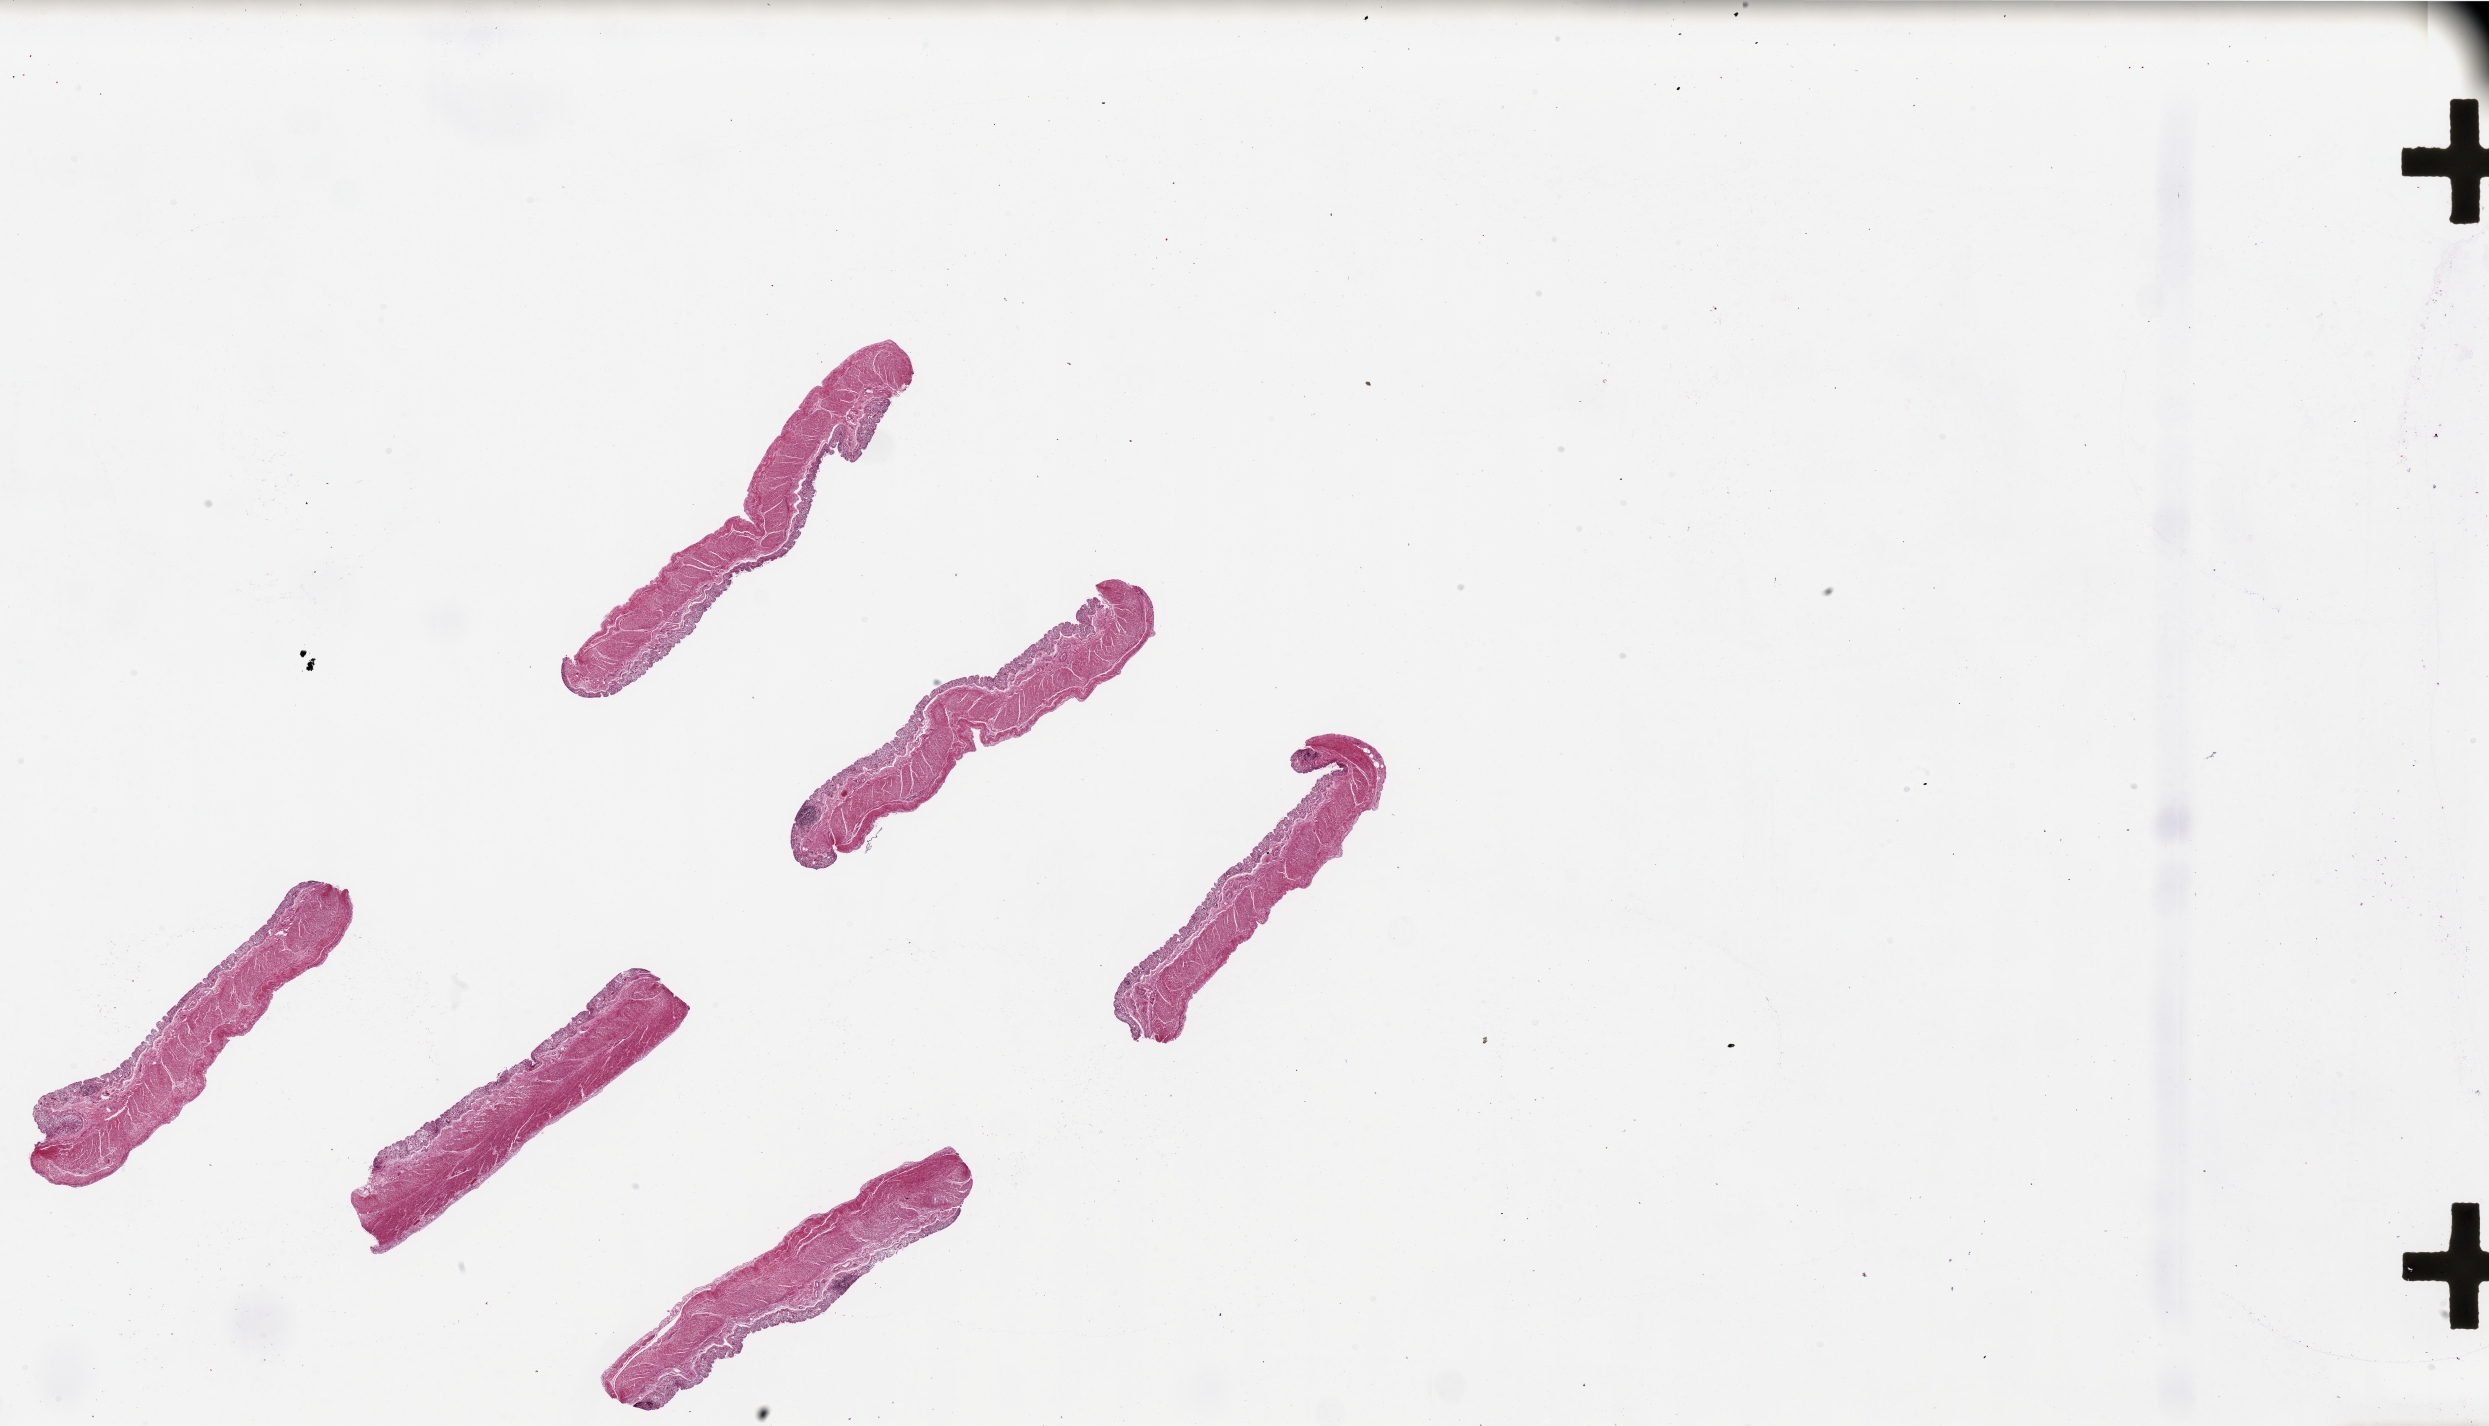
Haematoxylin and eosin whole-slide image, brightfield — shown as a low-resolution overview of the whole scanned area (about 39.4 x 22.6 mm). PAXgene-fixed, paraffin-embedded tissue. Sampled site (target tissue): transverse colon. Donor tissue sample.
Review note (as recorded): 8 pieces up to 7.4x1.2 mm; mucosa completely autolyzed, muscularis slight to moderate autolysis.